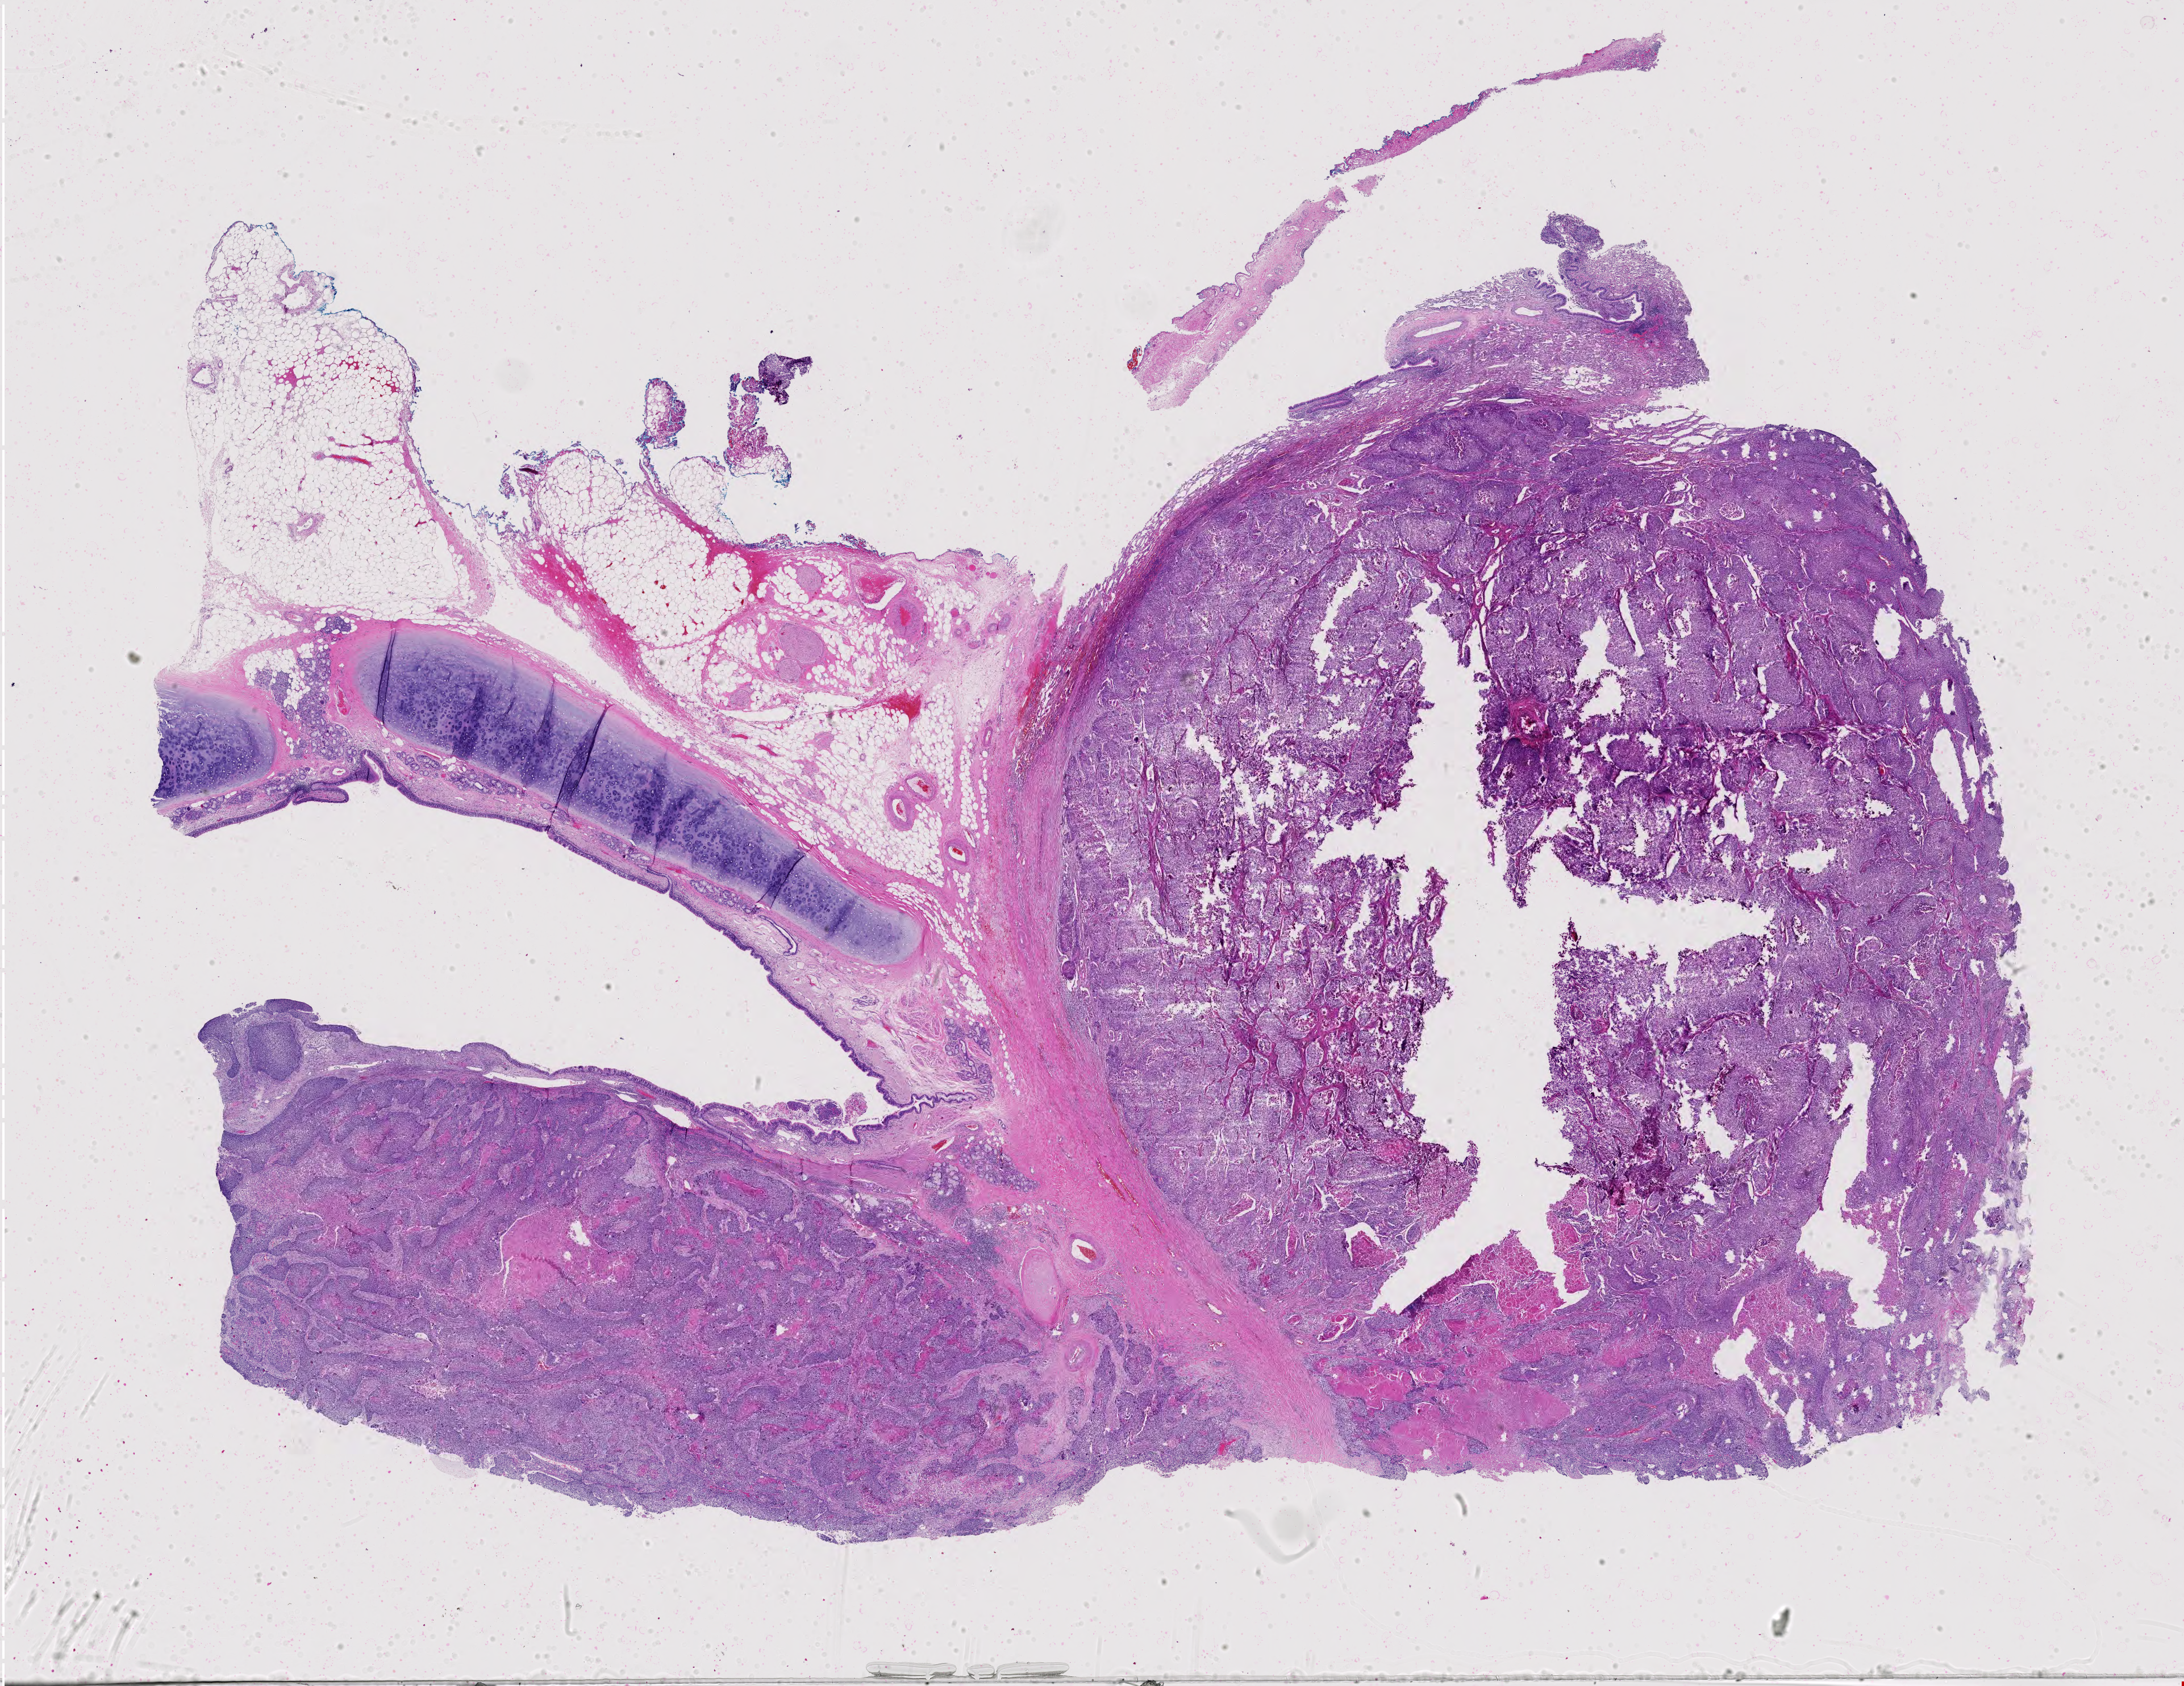
Digitized H&E tissue section (whole slide) — shown as a low-resolution overview of the whole scanned area (about 27.9 x 21.5 mm). FFPE section. Lung, primary tumour sample. Patient: male, age at initial diagnosis 61 years.
Histologic diagnosis: Squamous cell carcinoma, NOS. AJCC pathologic stage: IIA (7th edition).